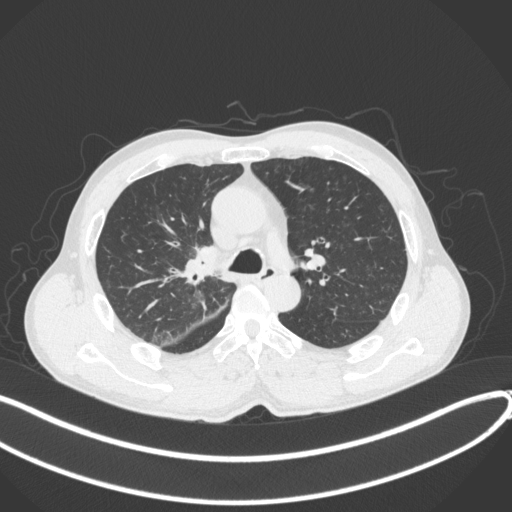
Chest CT, one axial slice. 120 kVp. Lung window (W 1500 / L -600 HU). 512 × 512 image matrix, field of view 400 × 400 mm. Male patient, age 53 years. Case-level facts recorded for this patient, not image findings: clinical TNM (as recorded): T1b N0 M0.
Annotated regions visible in this slice (rectangle marked by the reading radiologist):
- lung tumour (recorded histology: squamous cell carcinoma): box from (x=178, y=239) to (x=222, y=285) px